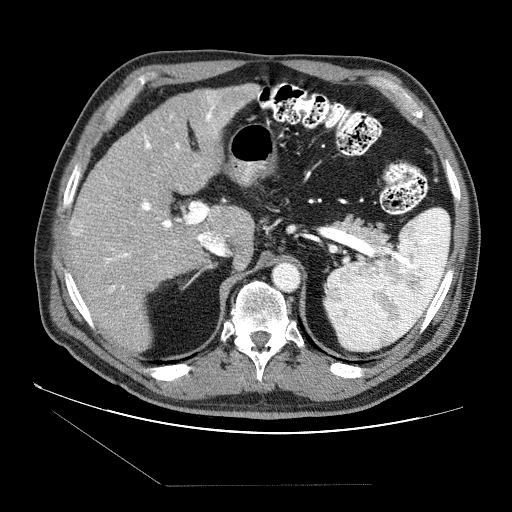
Contrast-enhanced abdominal CT (liver protocol), one axial slice. Position 50 of 87 along the scan axis. Reconstruction kernel STANDARD. 120 kVp. Soft-tissue window (W 400 / L 40 HU). 2.5 mm slice thickness. 512 × 512 image matrix, field of view 400 × 400 mm. Case-level facts recorded for this patient, not image findings: diagnosis: hepatocellular carcinoma (patient treated with transarterial chemoembolisation; whether this scan precedes or follows treatment is not stated here); TNM stage (as recorded): Stage-II; Child-Pugh class: B; tumour differentiation: no biopsy; tumour nodularity: multinodular.
Structures marked on this image (semi-automatically segmented with operator editing):
- liver parenchyma outside the tumour (the mass and vessels are separate outlines, so this box may not span the whole liver): bounding box [x1, y1, x2, y2] px = [66, 84, 260, 352]
- mass: [69, 213, 94, 236]
- liver vessels: [105, 92, 224, 293]